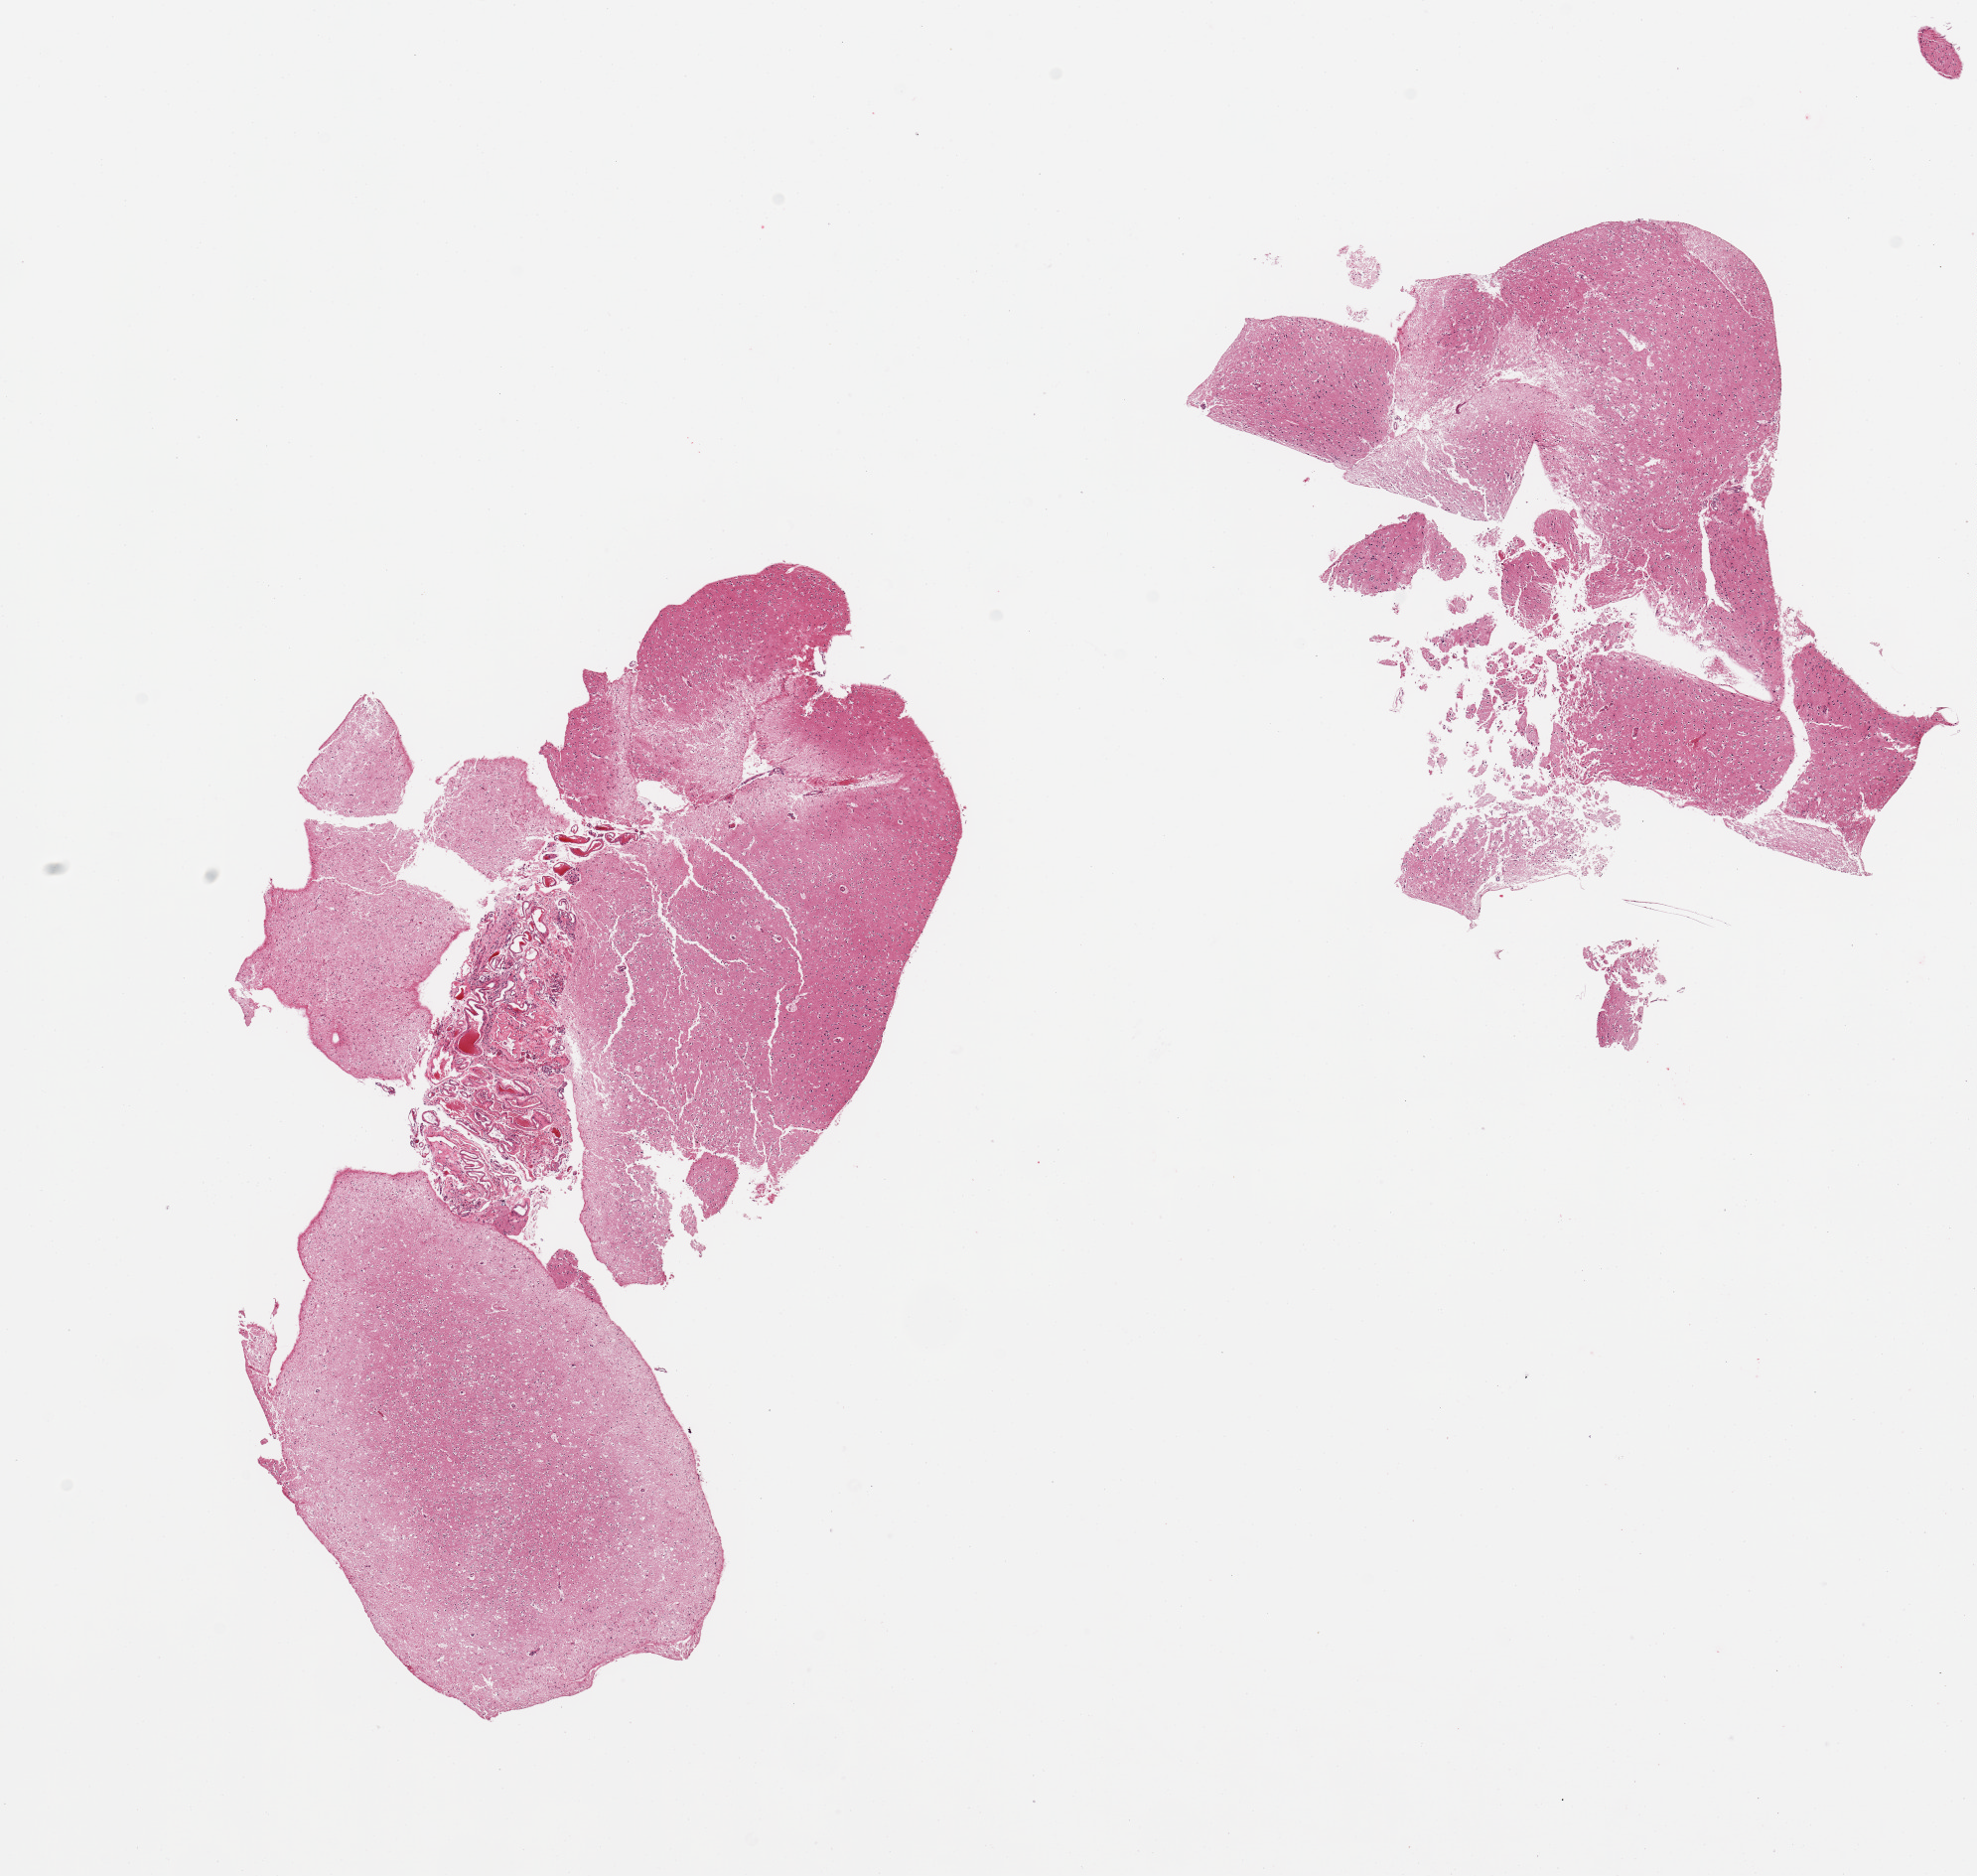
Digitized haematoxylin and eosin-stained section, low-resolution overview of the scanned area, about 15.8 x 14.9 mm (acquisition: 20x scan). PAXgene-fixed, paraffin-embedded tissue. Target tissue: cerebral cortex. Tissue donor sample. Male donor.
Review note (as recorded): 2 pieces; fragmented, focus of meninges.